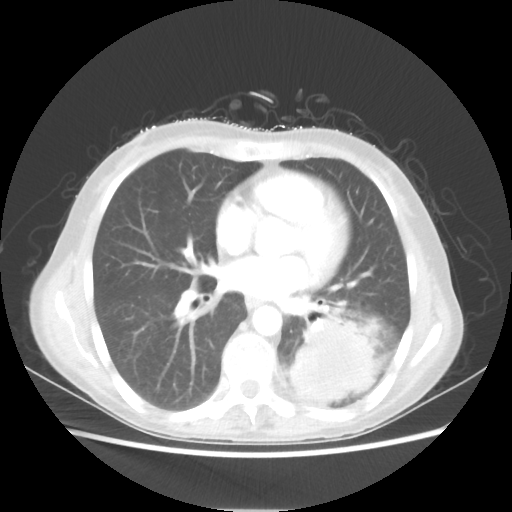
Chest CT, one axial slice; slice 26 of 56 in the series (ordered by position); reconstruction kernel STANDARD; 80 kVp; lung window (W 1500 / L -600 HU); 5 mm slice thickness; 512 × 512 image matrix. Patient: female, 53 years. Case-level facts recorded for this patient, not image findings: clinical TNM (as recorded): T3 N0 M0.
Annotated regions visible in this slice (rectangle marked by the reading radiologist):
- lung tumour (recorded histology: adenocarcinoma): bounding box (x1, y1, x2, y2) in pixels: (289, 318, 380, 403)